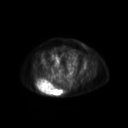
FDG PET of an extremity soft-tissue mass (from a PET/CT study), one axial slice; position 67 of 267 along the scan axis; 3.27 mm slice thickness; 128 × 128 image matrix, field of view 600 × 600 mm. Female patient, age 60 years. Case-level facts recorded for this patient, not image findings: histological type: spindle cell suggestive of myxofibrosarcoma; grade: intermediate; site of the primary tumour: right buttock.
Outlined on this slice (expert contour drawn on MRI and transferred to this co-registered scan by the dataset authors):
- gross tumour volume (mass): bounding box (x1, y1, x2, y2) in pixels: (36, 79, 63, 96)